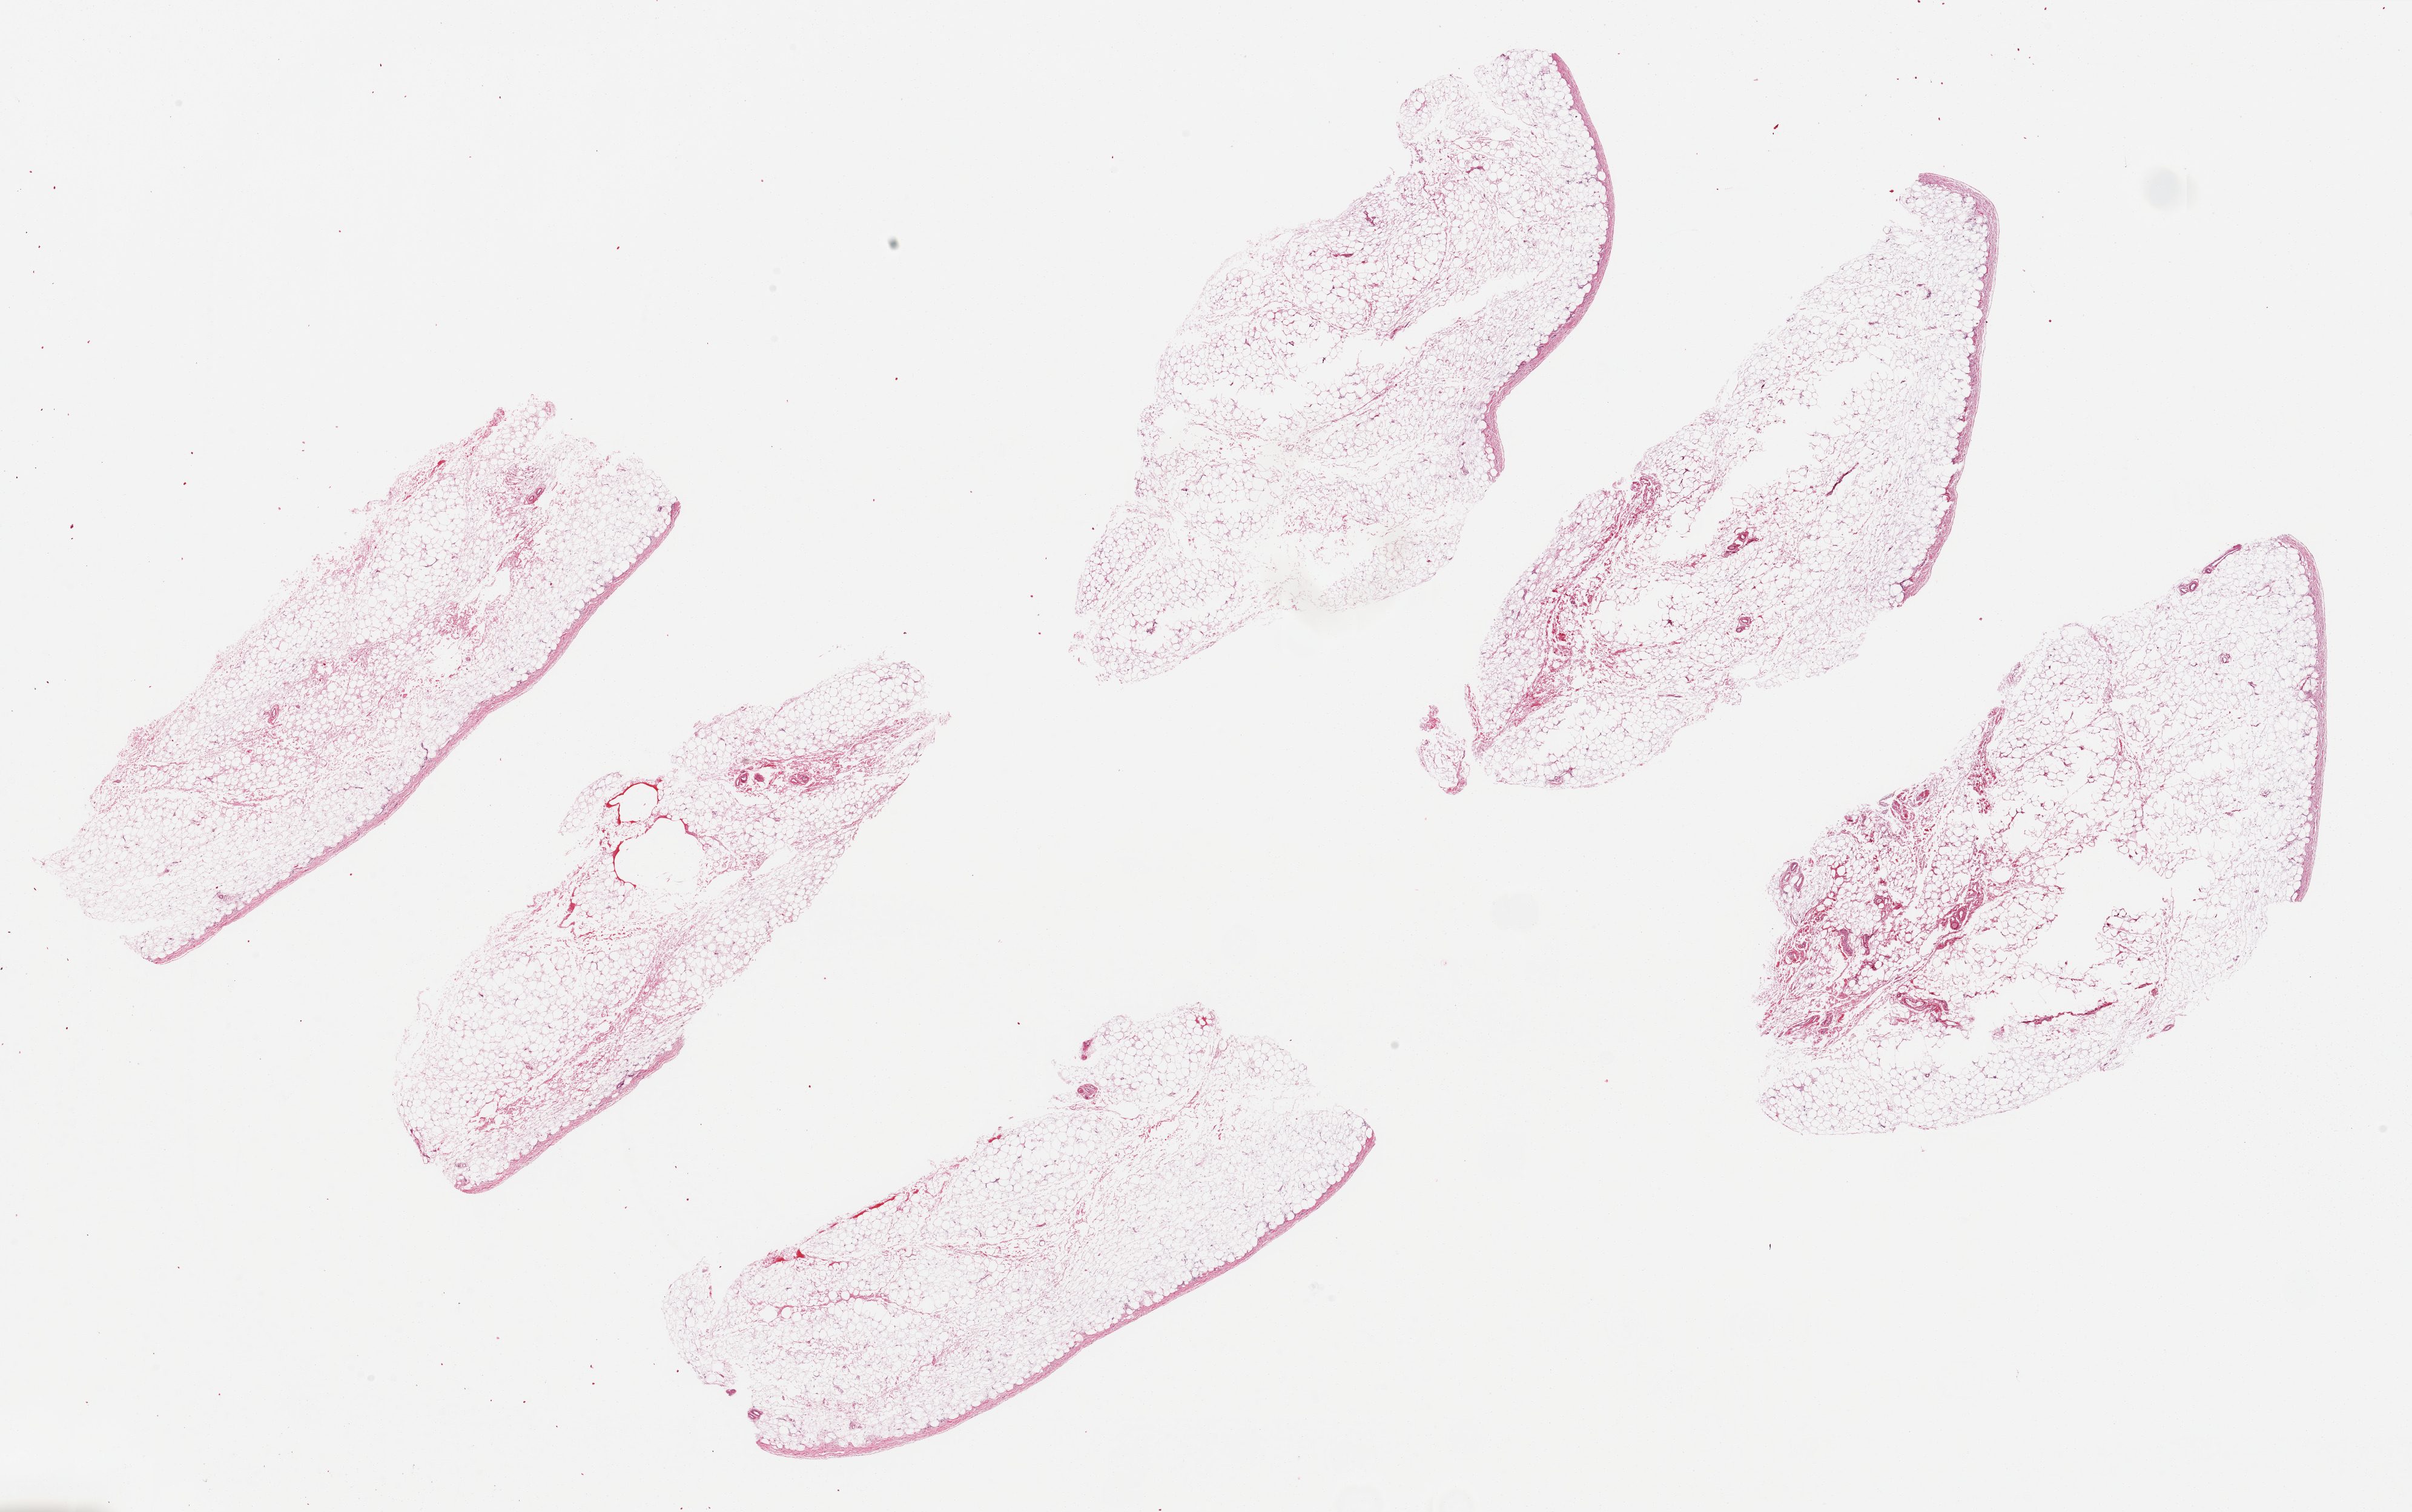
H&E whole-slide image, brightfield, whole scanned area (about 31.5 x 19.7 mm, acquisition: 20x scan) shown as a low-resolution overview, PAXgene-fixed paraffin-embedded (PFPE) section, target tissue: urinary bladder, tissue donor sample. Donor sex: male.
- pathologist's review note for this sample: 6 pieces of adipose tissue only; no urothelium or detrussor muscle is present